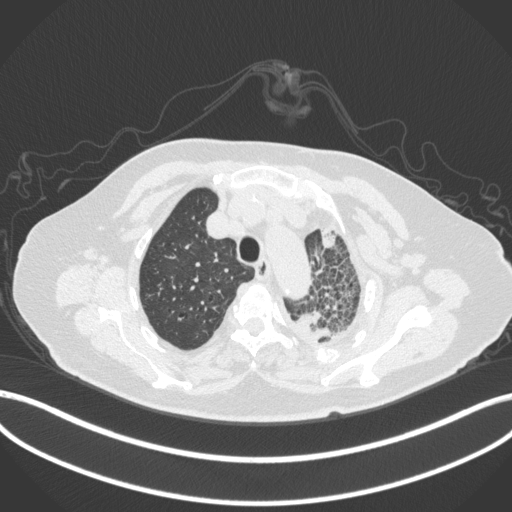
Chest CT, one axial slice; slice 318 of 399 in the series (ordered by position); reconstruction kernel B31f; lung window (W 1500 / L -600 HU); 1 mm slice thickness; 512 × 512 image matrix, field of view 400 × 400 mm. Patient: female, 75 years. From the clinical record (not read from this slice): clinical TNM (as recorded): T3 N3 M1.
Annotated regions visible in this slice (bounding box drawn by a radiologist):
- lung tumour (recorded histology: adenocarcinoma): box from (x=287, y=309) to (x=338, y=352) px